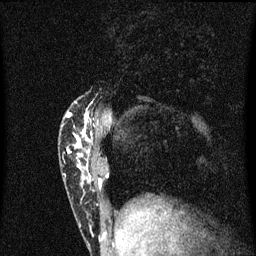
Breast MRI (dynamic contrast-enhanced), one sagittal slice. Position 15 of 60 along the scan axis. Dynamic contrast-enhanced series, image 2 of 3 at this slice position (ordered by acquisition). 1.5 T. TE 4.2 ms, TR 8.4 ms. 2 mm slice thickness. 256 × 256 image matrix, field of view 200 × 200 mm. Female patient, age 40 years.
Annotated regions visible in this slice (semi-automatically segmented with operator editing):
- analysis volume of interest (the breast-tissue region the enhancement analysis was run in; not a lesion): box from (x=60, y=102) to (x=103, y=203) px
- tumour enhancement mask (voxels above the 70 % enhancement threshold inside the analysis volume of interest): (x=67, y=112)–(x=92, y=179)